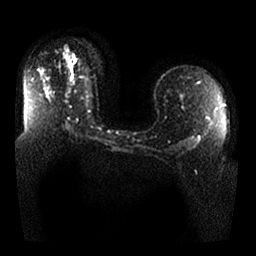
Breast MRI, one axial slice; slice 16 of 25 in the series (ordered by position); diffusion-weighted series; image 2 of 4 stored at this slice position (different b-values; order by instance number); 1.5 T; 256 × 256 image matrix, field of view 360 × 360 mm. Female patient.
Outlined on this slice (outlined manually by an expert reader):
- tumour on diffusion-weighted imaging: bounding box (x1, y1, x2, y2) in pixels: (66, 53, 72, 67)